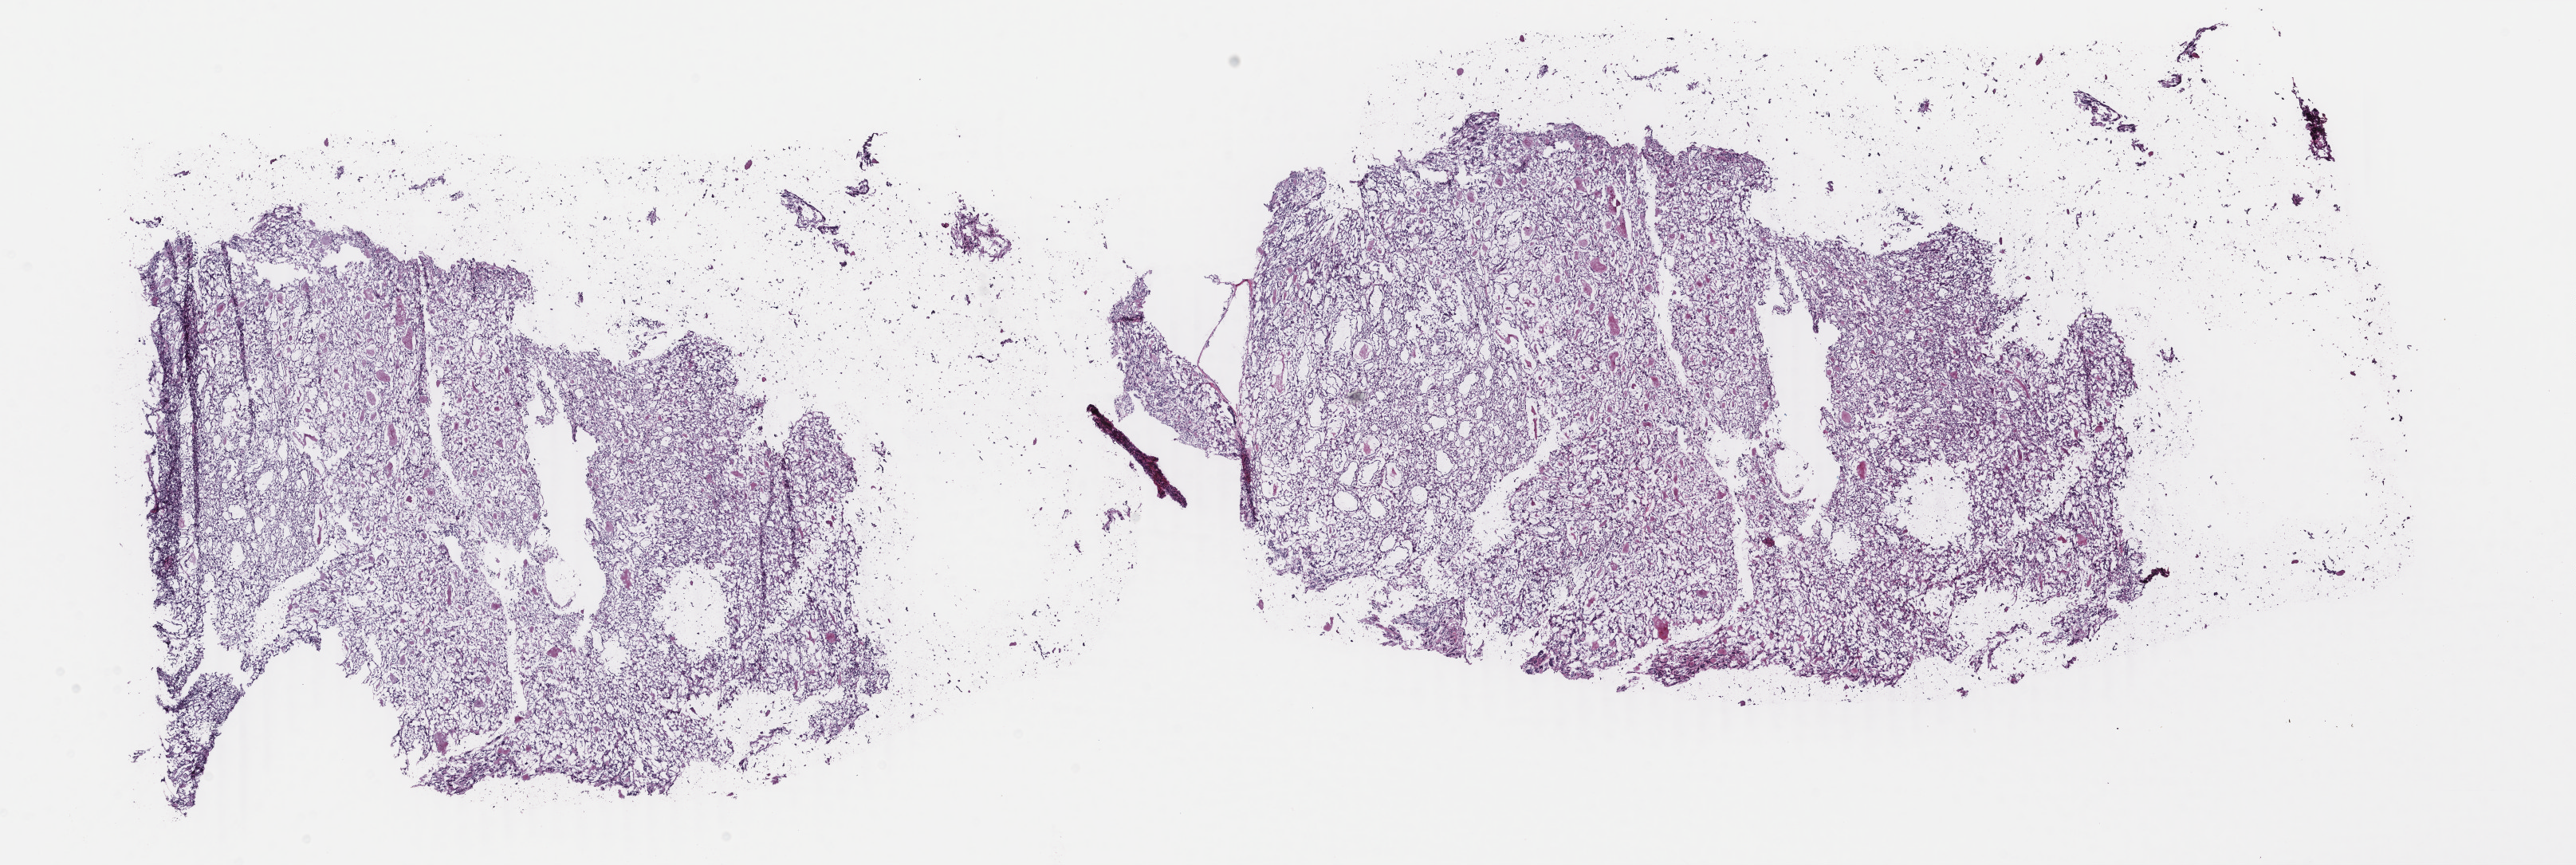
Digitized H&E-stained tissue section (whole slide), shown as a low-resolution overview of the whole scanned area (about 25.7 x 8.6 mm), frozen section from the bottom of the tissue portion, thyroid, primary tumour sample. Female, age 45 years at initial diagnosis. Composition of this section per pathologist review: tumour cells 100%, tumour nuclei 97%, normal cells 0%, stromal cells 0%, necrosis 0%. Infiltration values recorded for this section: lymphocyte infiltration 0%, monocyte infiltration 0%, neutrophil infiltration 0%.
• TNM: T1b N0 M0
• lymph nodes positive (case pathology): 0 of 3 examined
• diagnosis: Papillary carcinoma, follicular variant (thyroid gland)
• AJCC pathologic stage: I (7th edition)
• laterality: left